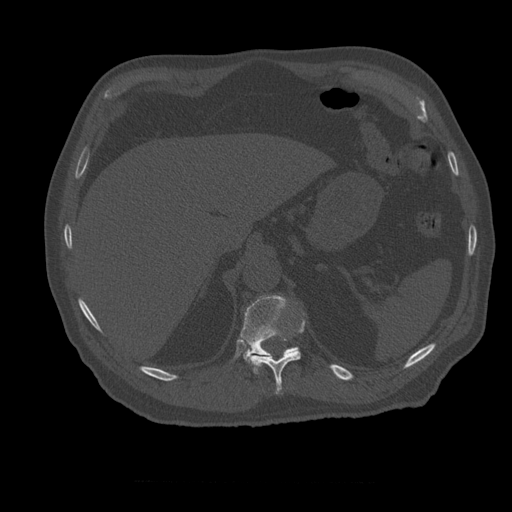
CT including the spine, one axial slice. Slice 274 of 399 in the series (ordered by position). 120 kVp. Bone window (W 1800 / L 400 HU). 1.25 mm slice thickness. 512 × 512 image matrix. Patient age 73 years. From the clinical record (not read from this slice): primary cancer: prostate; vertebrae with lytic lesions (as recorded): L2.
Structures marked on this image (semi-automatically segmented with operator editing):
- T11 vertebra: bounding box [x1, y1, x2, y2] px = [249, 320, 305, 394]
- T12 vertebra: [241, 295, 300, 363]